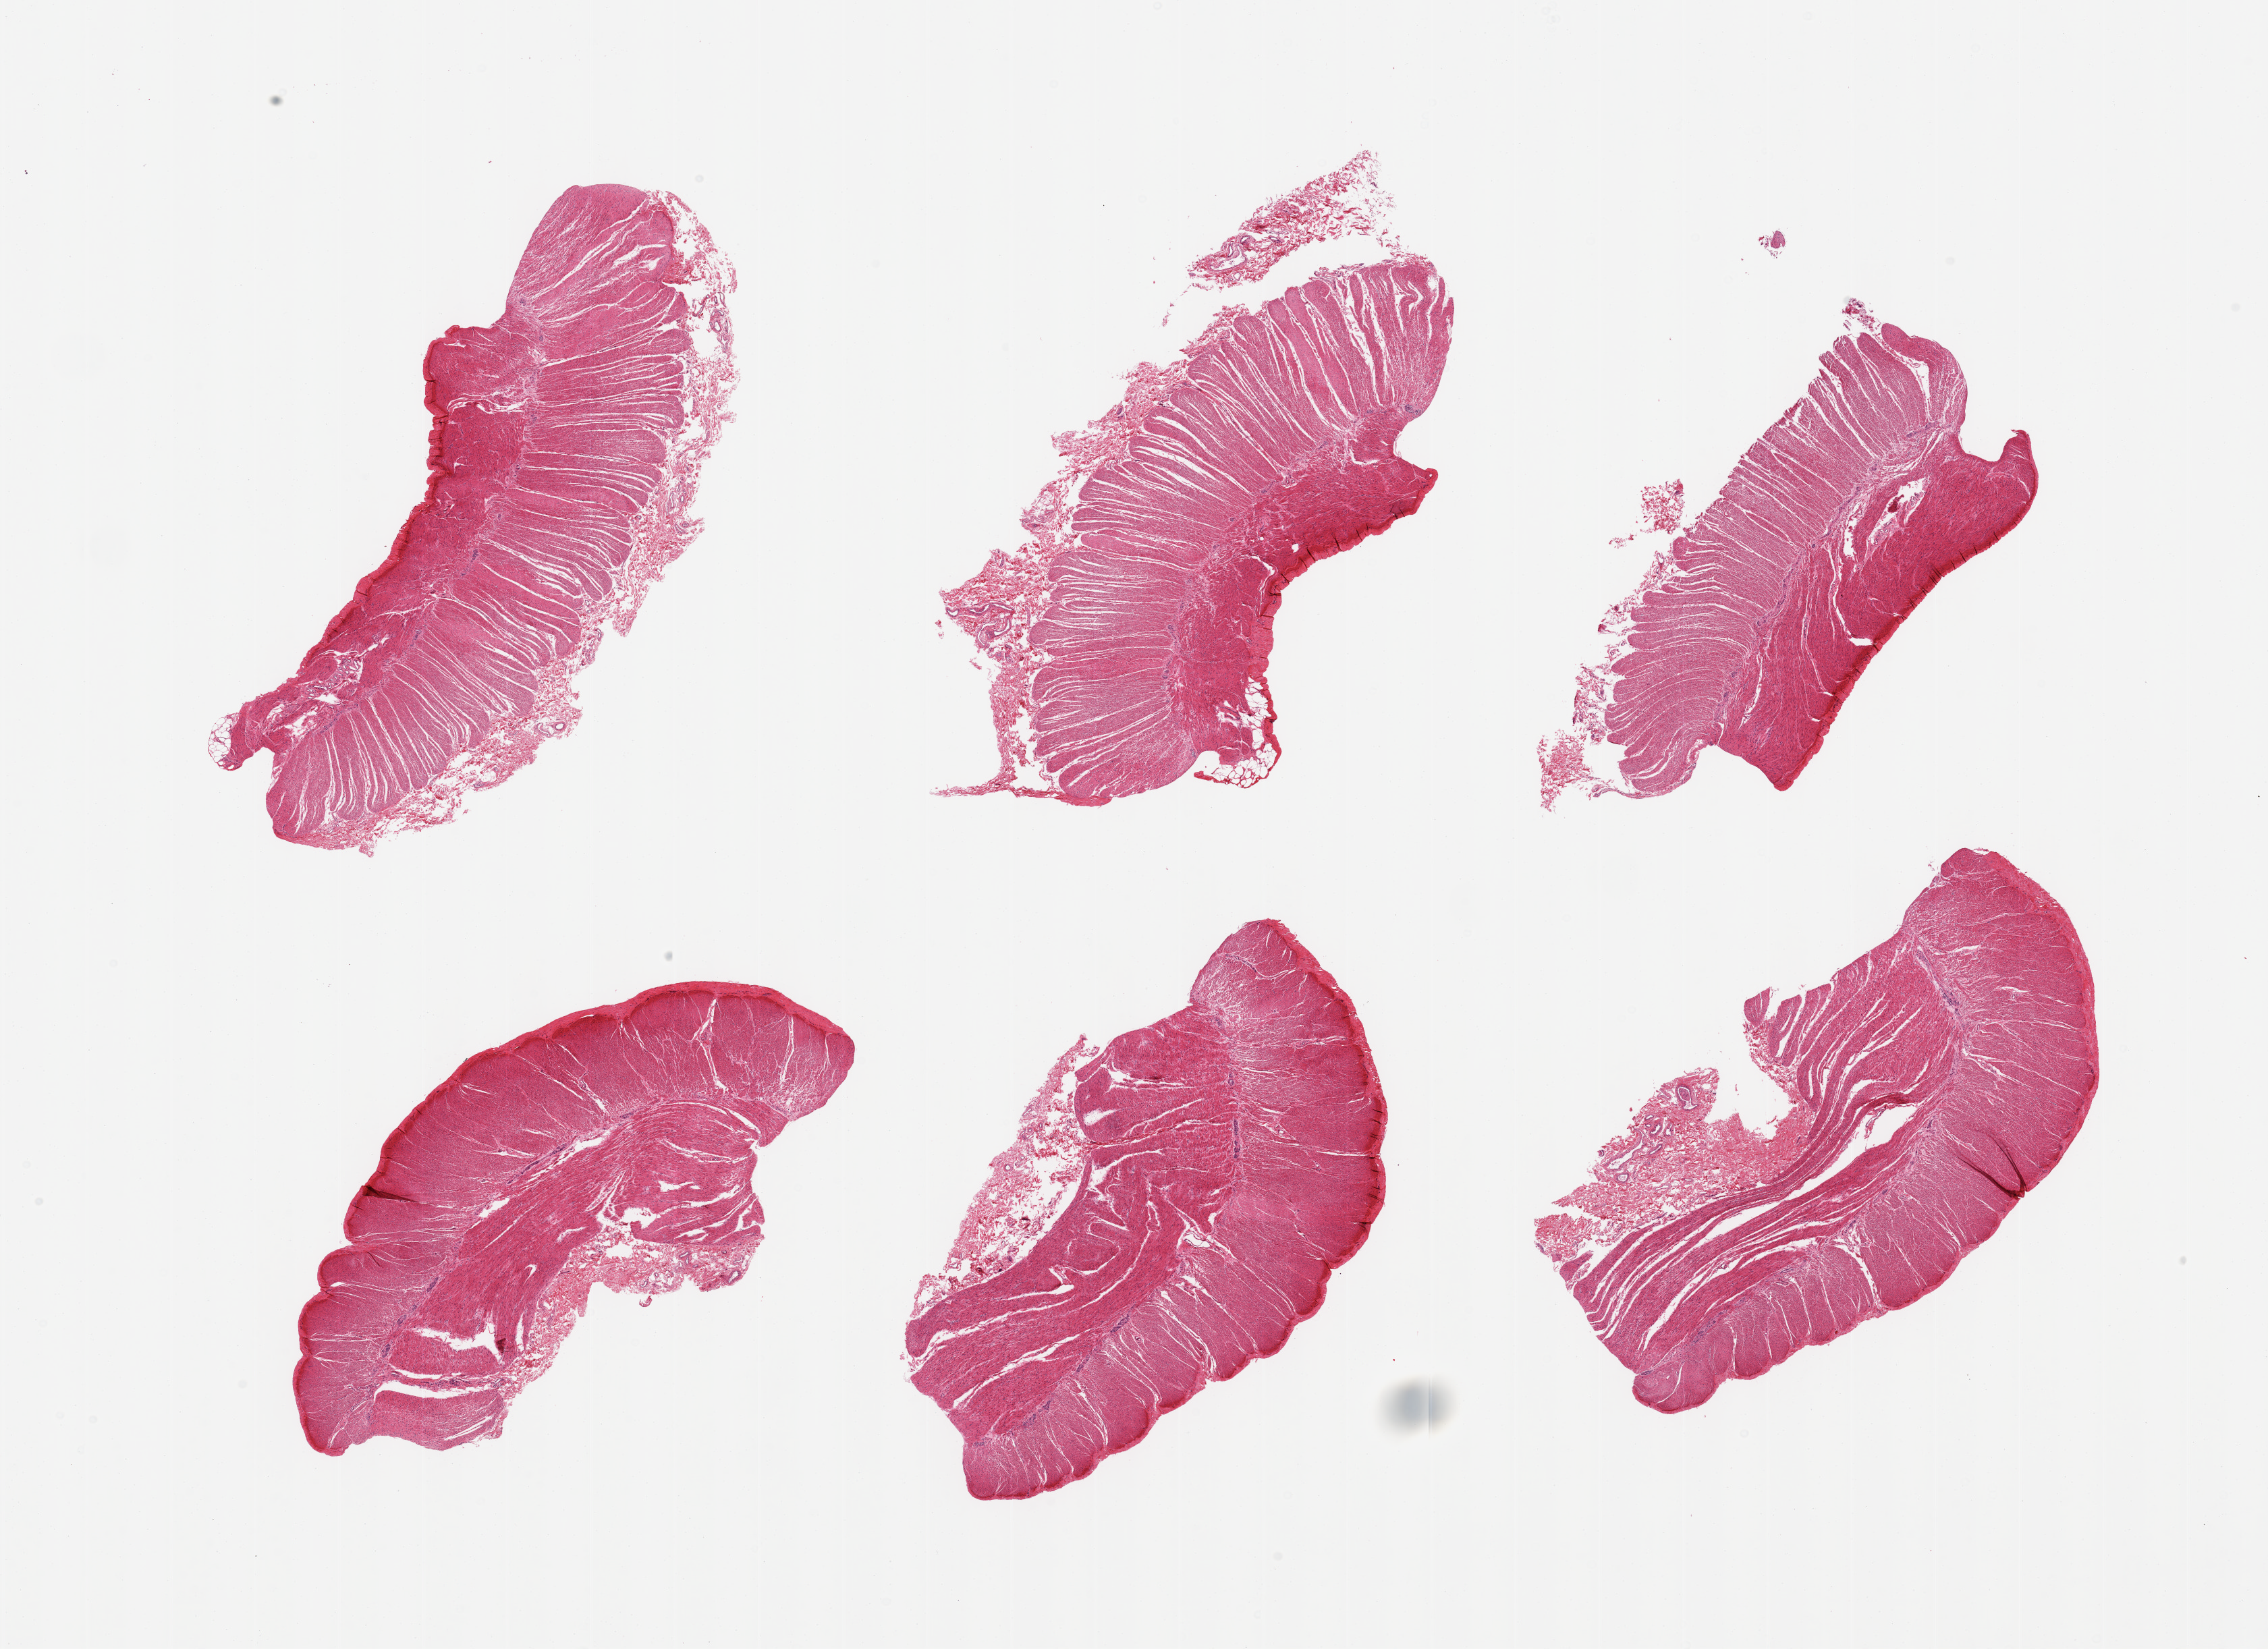
Digitized hematoxylin and eosin (H&E)-stained section, brightfield — a low-resolution overview of the entire scanned area, about 26.6 x 19.3 mm (from a 20x scan). PAXgene-fixed paraffin-embedded (PFPE) section. Sampled site (target tissue): sigmoid colon. Donor tissue sample. Donor: male.
Pathologist's review note for this sample: 6 pieces; target muscularis.